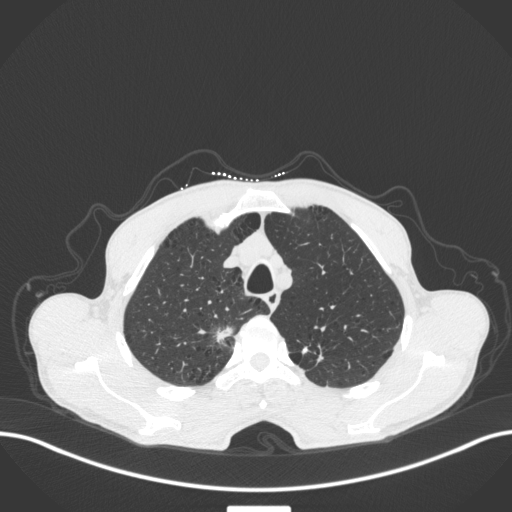
Chest CT, one axial slice. Slice 350 of 445 in the series (ordered by position). Reconstruction kernel B31f. 120 kVp. Lung window (W 1500 / L -600 HU). 1 mm slice thickness. 512 × 512 image matrix. Patient: male, 70 years. From the clinical record (not read from this slice): clinical TNM (as recorded): T1a N0 M0.
Outlined on this slice (bounding box drawn by a radiologist):
- lung tumour (recorded histology: adenocarcinoma): bounding box [x1, y1, x2, y2] px = [198, 319, 242, 348]